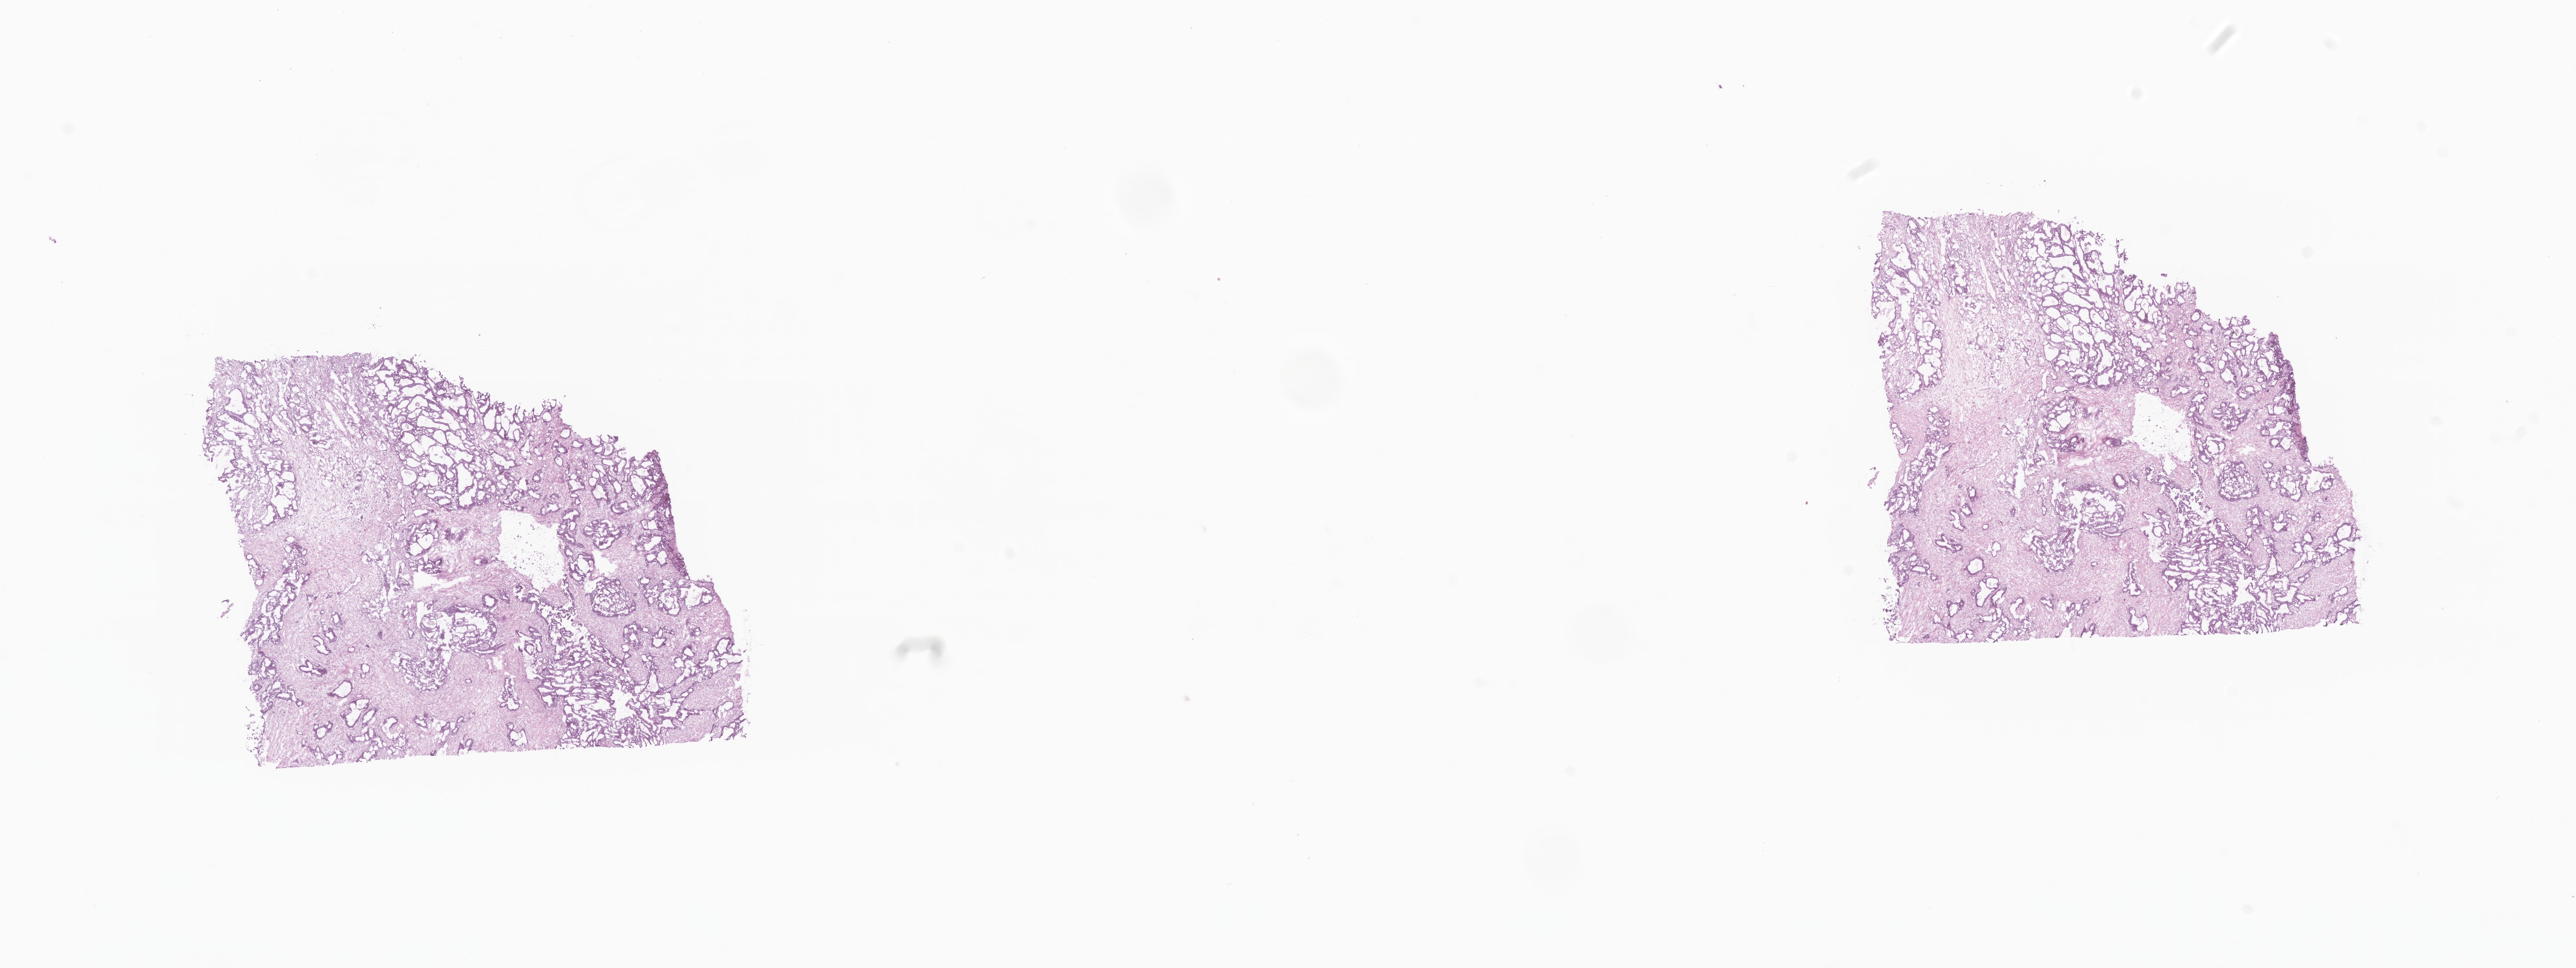
Hematoxylin and eosin (H&E) whole-slide image, whole scanned area (about 23.2 x 8.7 mm) shown as a low-resolution overview, frozen section, specimen: metastatic tumor tissue, resected from liver. Male patient; age at initial diagnosis 66 years. Composition of this section per pathologist review: tumor cells 75%, tumor nuclei 75%, stromal cells 25%, necrosis 0%, normal cells 0%. Inflammatory infiltration, as recorded: lymphocyte infiltration 5%, monocyte infiltration 3%, neutrophil infiltration 7%.
- patient diagnosis (primary): Adenocarcinoma, NOS